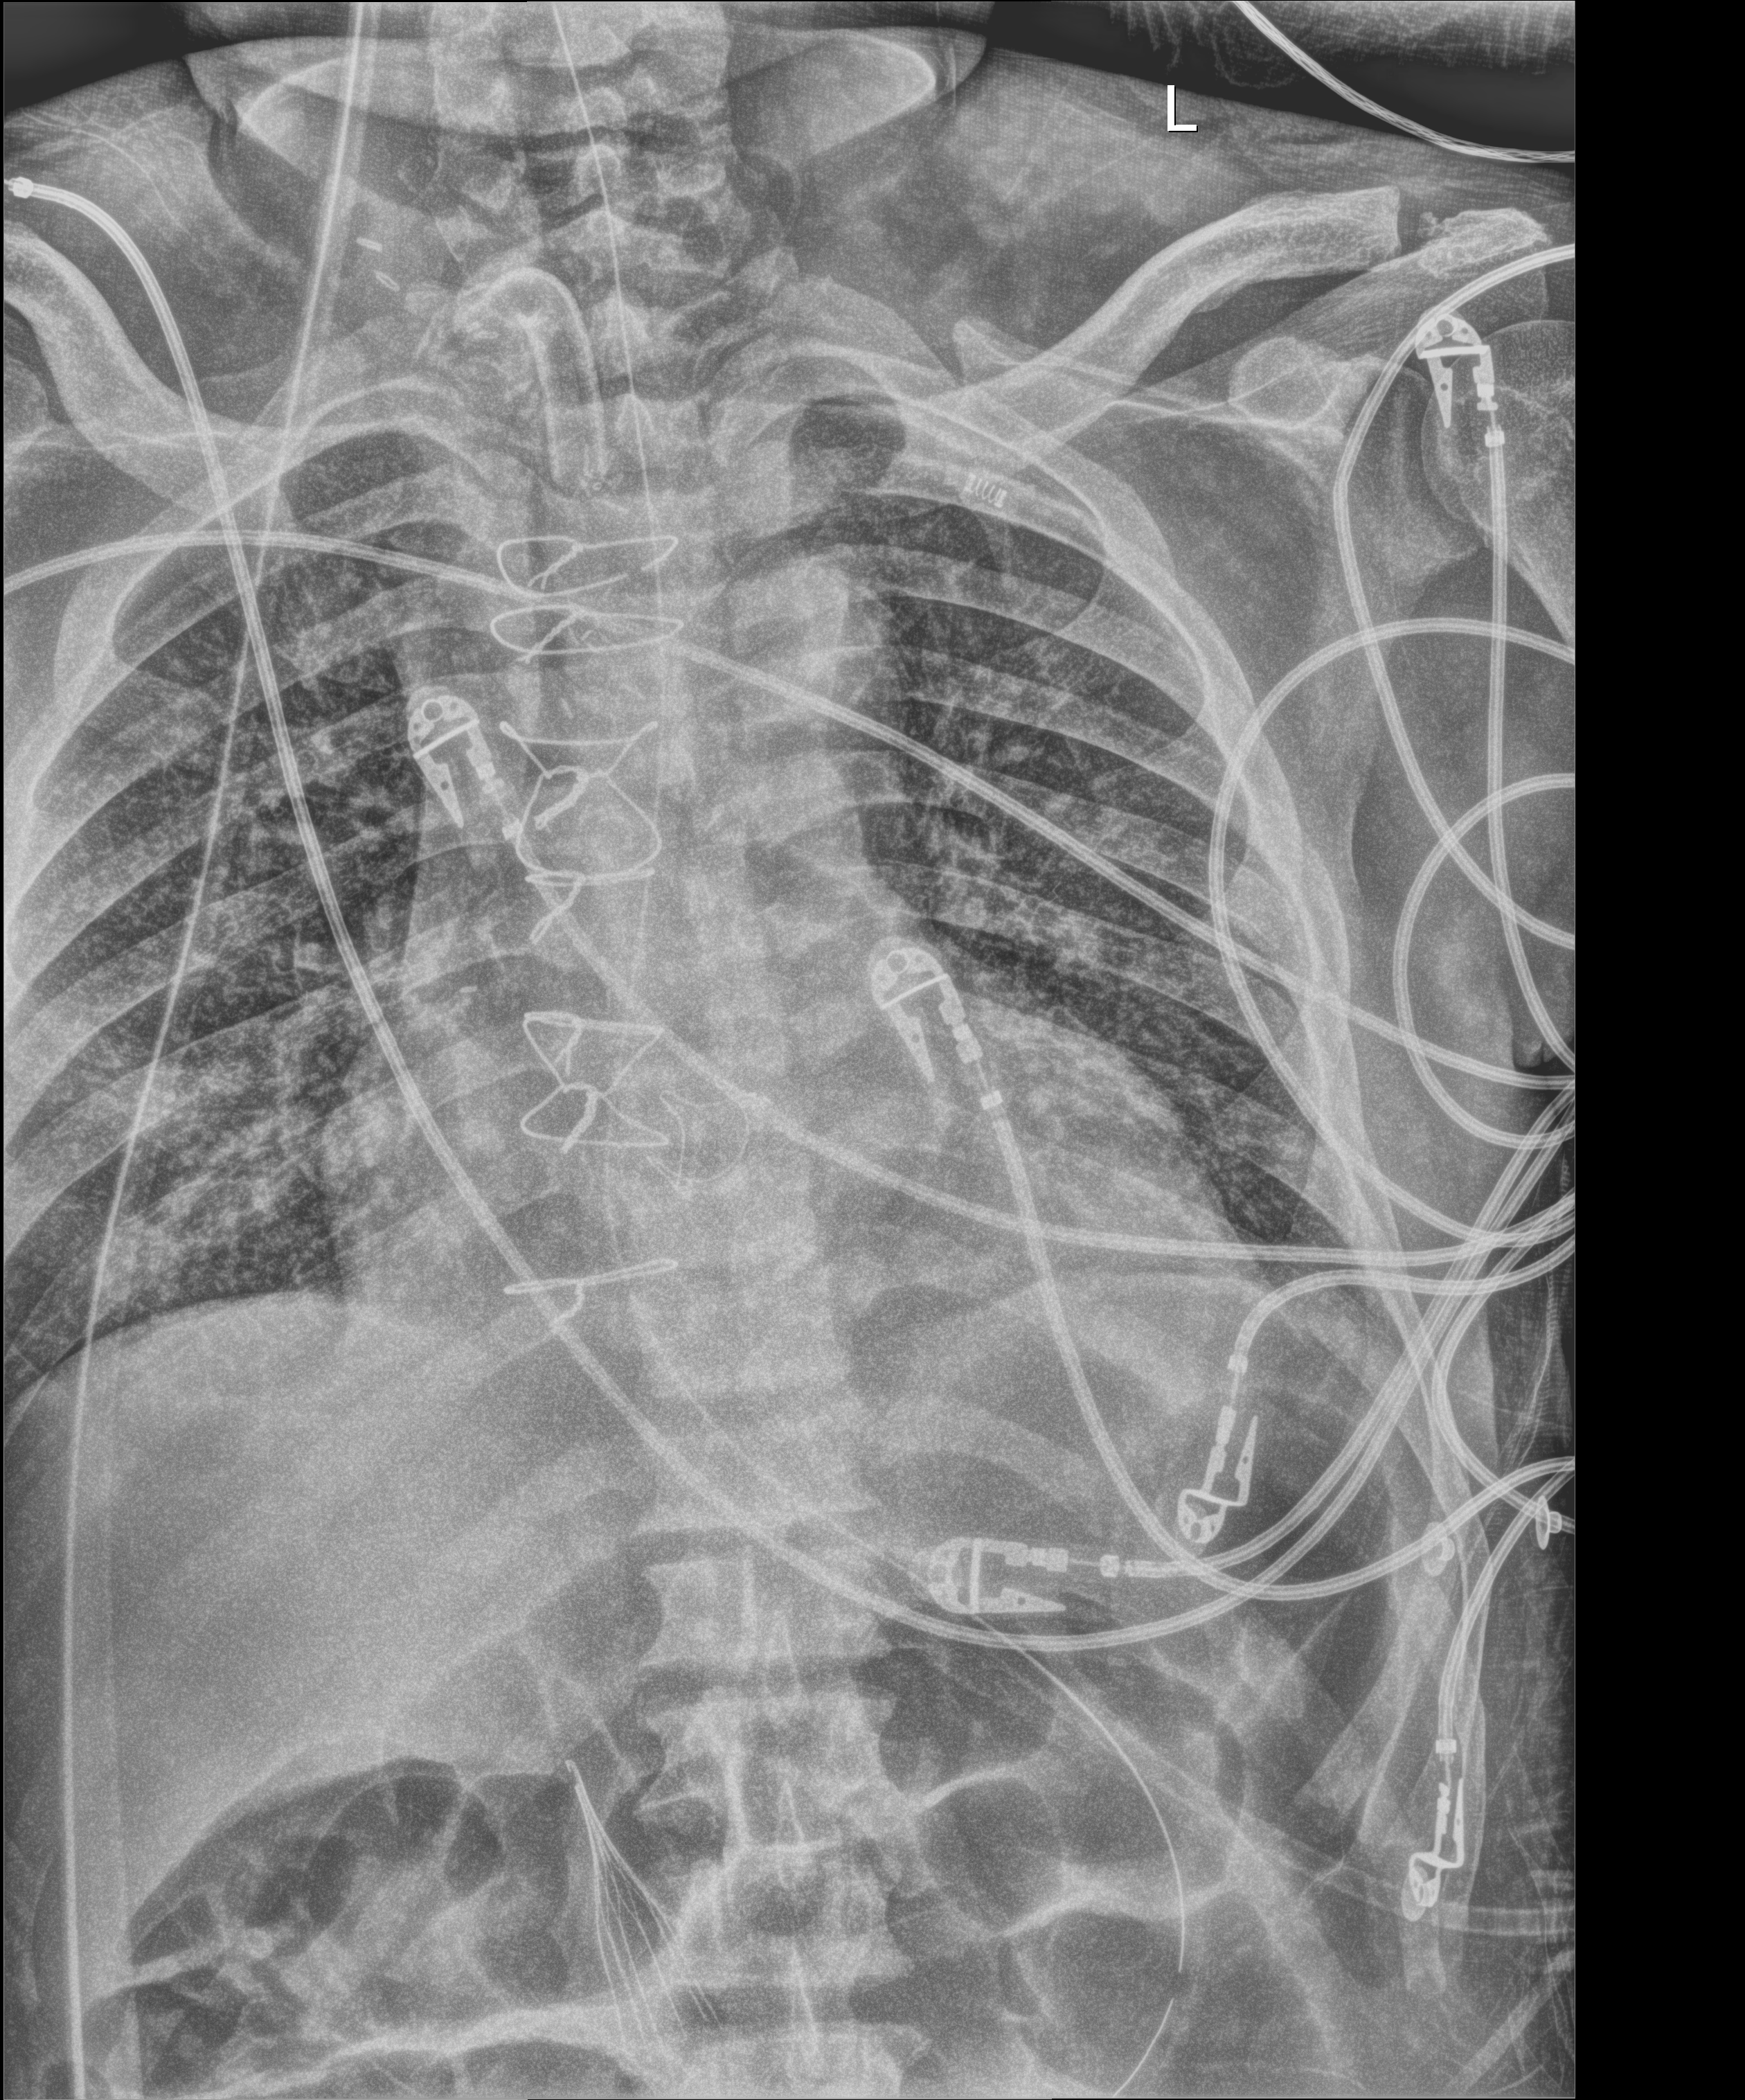
Portable chest radiograph. Male patient hospitalised with COVID-19, age 60–74 years.
Hospital-stay facts (about this admission, not read from this image; timing relative to this image not recorded):
- smoking status (admission record): never
- admitted to intensive care during this hospital stay: yes